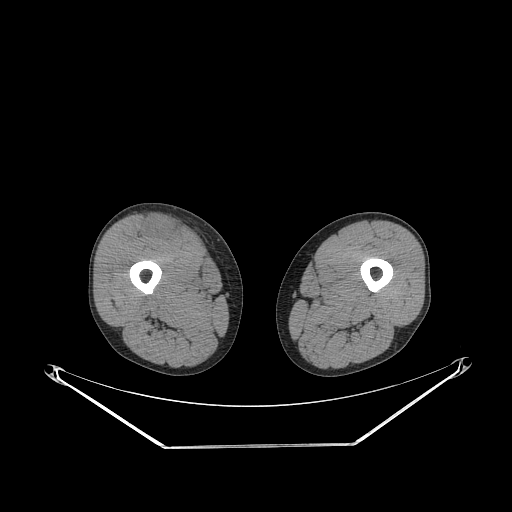
CT of an extremity soft-tissue mass (from a PET/CT study), one axial slice; slice 247 of 311 in the series (ordered by position); reconstruction kernel STANDARD; soft-tissue window (W 400 / L 40 HU); 3.75 mm slice thickness; 512 × 512 image matrix, field of view 500 × 500 mm. Male patient. From the clinical record (not read from this slice): histological type: pleiomorphic leiomyosarcoma; grade: intermediate; site of the primary tumour: right thigh.
Annotated regions visible in this slice (expert contour drawn on MRI and transferred to this co-registered scan by the dataset authors):
- gross tumour volume including surrounding oedema: bounding box [x1, y1, x2, y2] px = [146, 217, 181, 243]